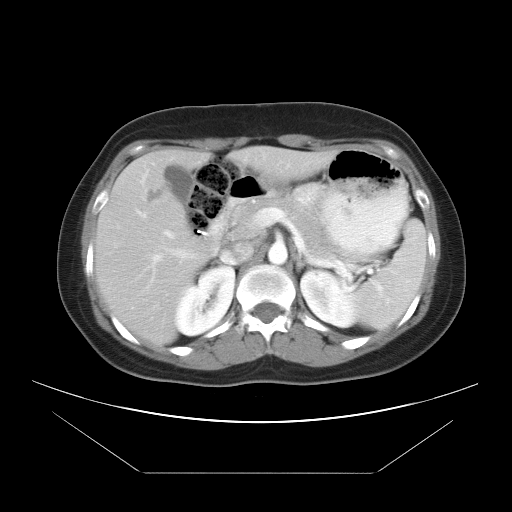
Contrast-enhanced abdominal CT, one axial slice; position 23 of 34 along the scan axis; reconstruction kernel STANDARD; 120 kVp; intravenous contrast given; soft-tissue window (W 400 / L 40 HU); 7.5 mm slice thickness; 512 × 512 image matrix, field of view 410 × 410 mm. Female patient, age 38 years. Case-level facts recorded for this patient, not image findings: diagnosis: colorectal cancer liver metastases, imaged before liver resection; multiple liver metastases: yes; largest metastasis: 3.1 cm; disease in both lobes: no.
Structures marked on this image (manually delineated by an expert):
- liver: bounding box [x1, y1, x2, y2] px = [95, 146, 335, 344]
- planned liver remnant (the part of the liver to remain after resection): [203, 146, 336, 249]
- portal vein (with intrahepatic branches): [135, 208, 221, 284]
- liver metastasis: [144, 185, 167, 205]